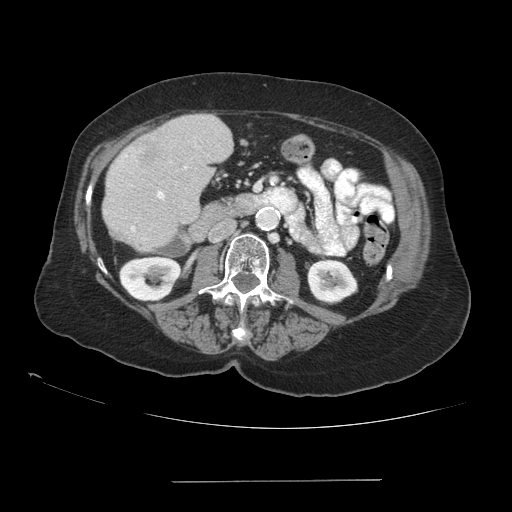
Contrast-enhanced abdominal CT (liver protocol), one axial slice. Slice 31 of 89 in the series (ordered by position). Reconstruction kernel STANDARD. Soft-tissue window (W 400 / L 40 HU). 512 × 512 image matrix, field of view 400 × 400 mm. From the clinical record (not read from this slice): diagnosis: hepatocellular carcinoma (patient treated with transarterial chemoembolisation; whether this scan precedes or follows treatment is not stated here); TNM stage (as recorded): Stage-IVA; Child-Pugh class: A; tumour differentiation: poorly differentiated.
Outlined on this slice (semi-automatic segmentation, software-assisted and operator-edited):
- liver parenchyma outside the tumour (the mass and vessels are separate outlines, so this box may not span the whole liver): box from (x=102, y=114) to (x=232, y=250) px
- mass: (x=125, y=136)–(x=161, y=167)
- liver vessels: (x=131, y=166)–(x=187, y=231)